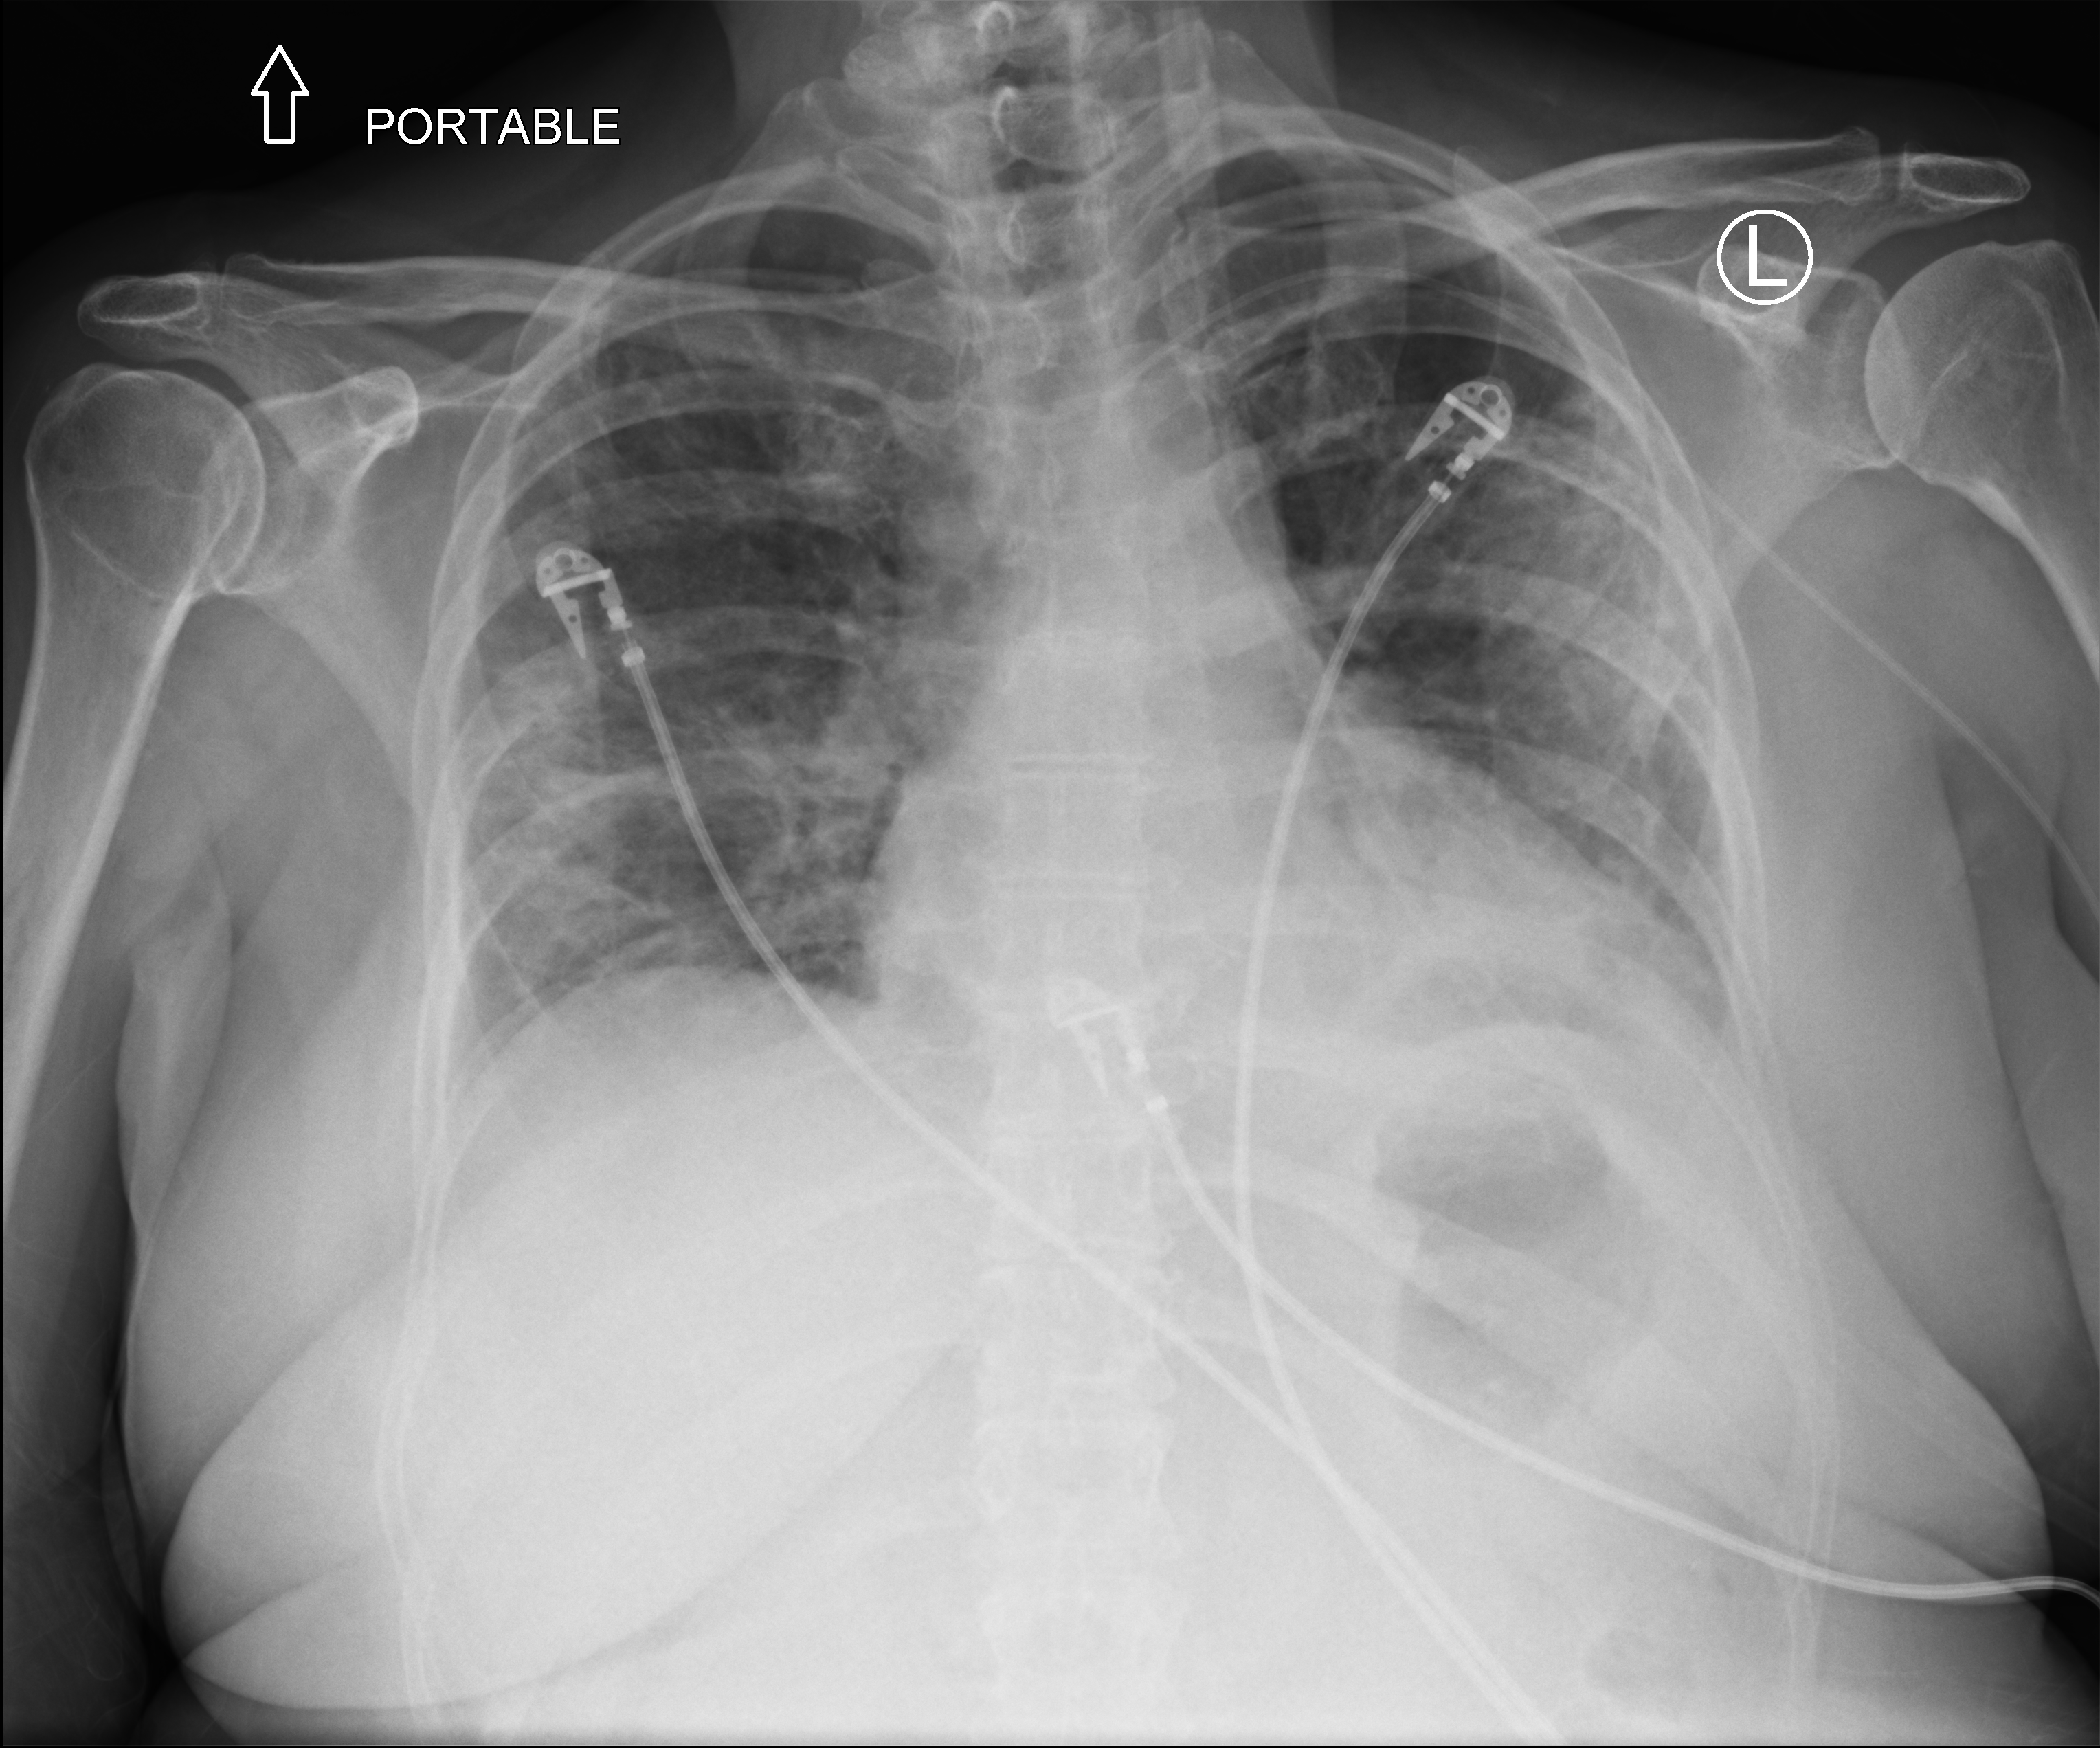
Portable chest radiograph, anteroposterior (AP) projection. Patient hospitalised with COVID-19; female, aged 18–59 years.
From the hospital-stay record, not from the radiograph (when in the stay this image was taken is not recorded): admitted to intensive care during this hospital stay: yes; mechanically ventilated during this hospital stay: yes; length of hospital stay: 20 days.